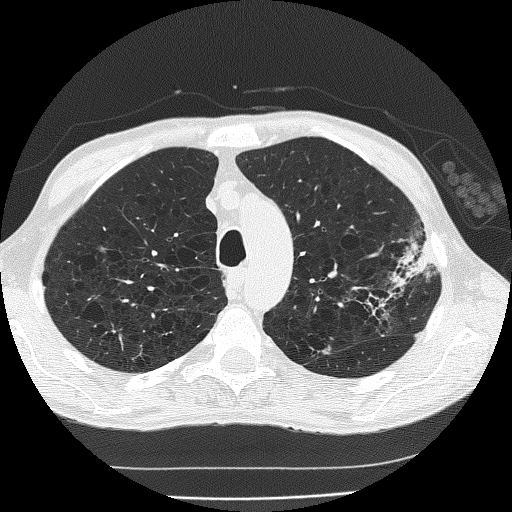
Low-dose screening chest CT, axial slice, second screening round (one year after baseline), lung window (W 1500 / L -600 HU), slice 45 of 185 in the series, 512 × 512 image matrix. Male participant, aged 60 years at enrolment. Current smoker at enrolment.
- Lesion marked by an expert reader, box from (x=346, y=241) to (x=441, y=336) px.
- The screening reader recorded 2 non-calcified nodules or masses ≥4 mm on this exam; which of them this box marks is not recorded.
- Official screen result: positive, other.